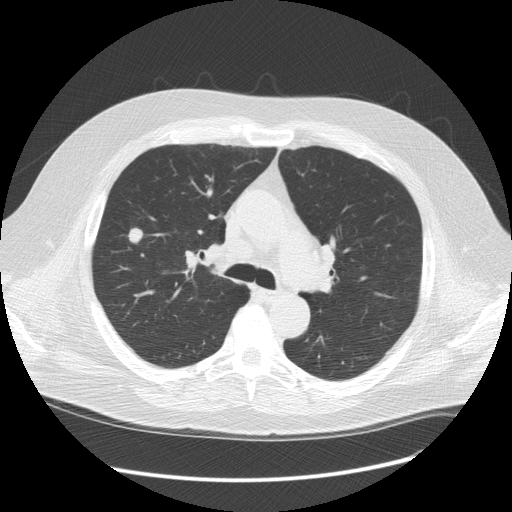
Low-dose screening chest CT, axial slice, third annual screen, lung window (W 1500 / L -600 HU), 2.5 mm slice thickness, 512 × 512 image matrix. Male participant, aged 61 years at enrolment. Current smoker at enrolment.
• Lesion marked by an expert reader, bounding box (x1, y1, x2, y2) in pixels: (109, 217, 151, 256).
• Reader record for this screening exam (exam-level; its link to the box is not recorded): non-calcified nodule or mass ≥4 mm, right upper lobe, 13 × 11 mm, spiculated (stellate) margins, soft tissue attenuation, pre-existing on the prior screen: yes; interval growth: yes.
• Official screen result: positive, other.